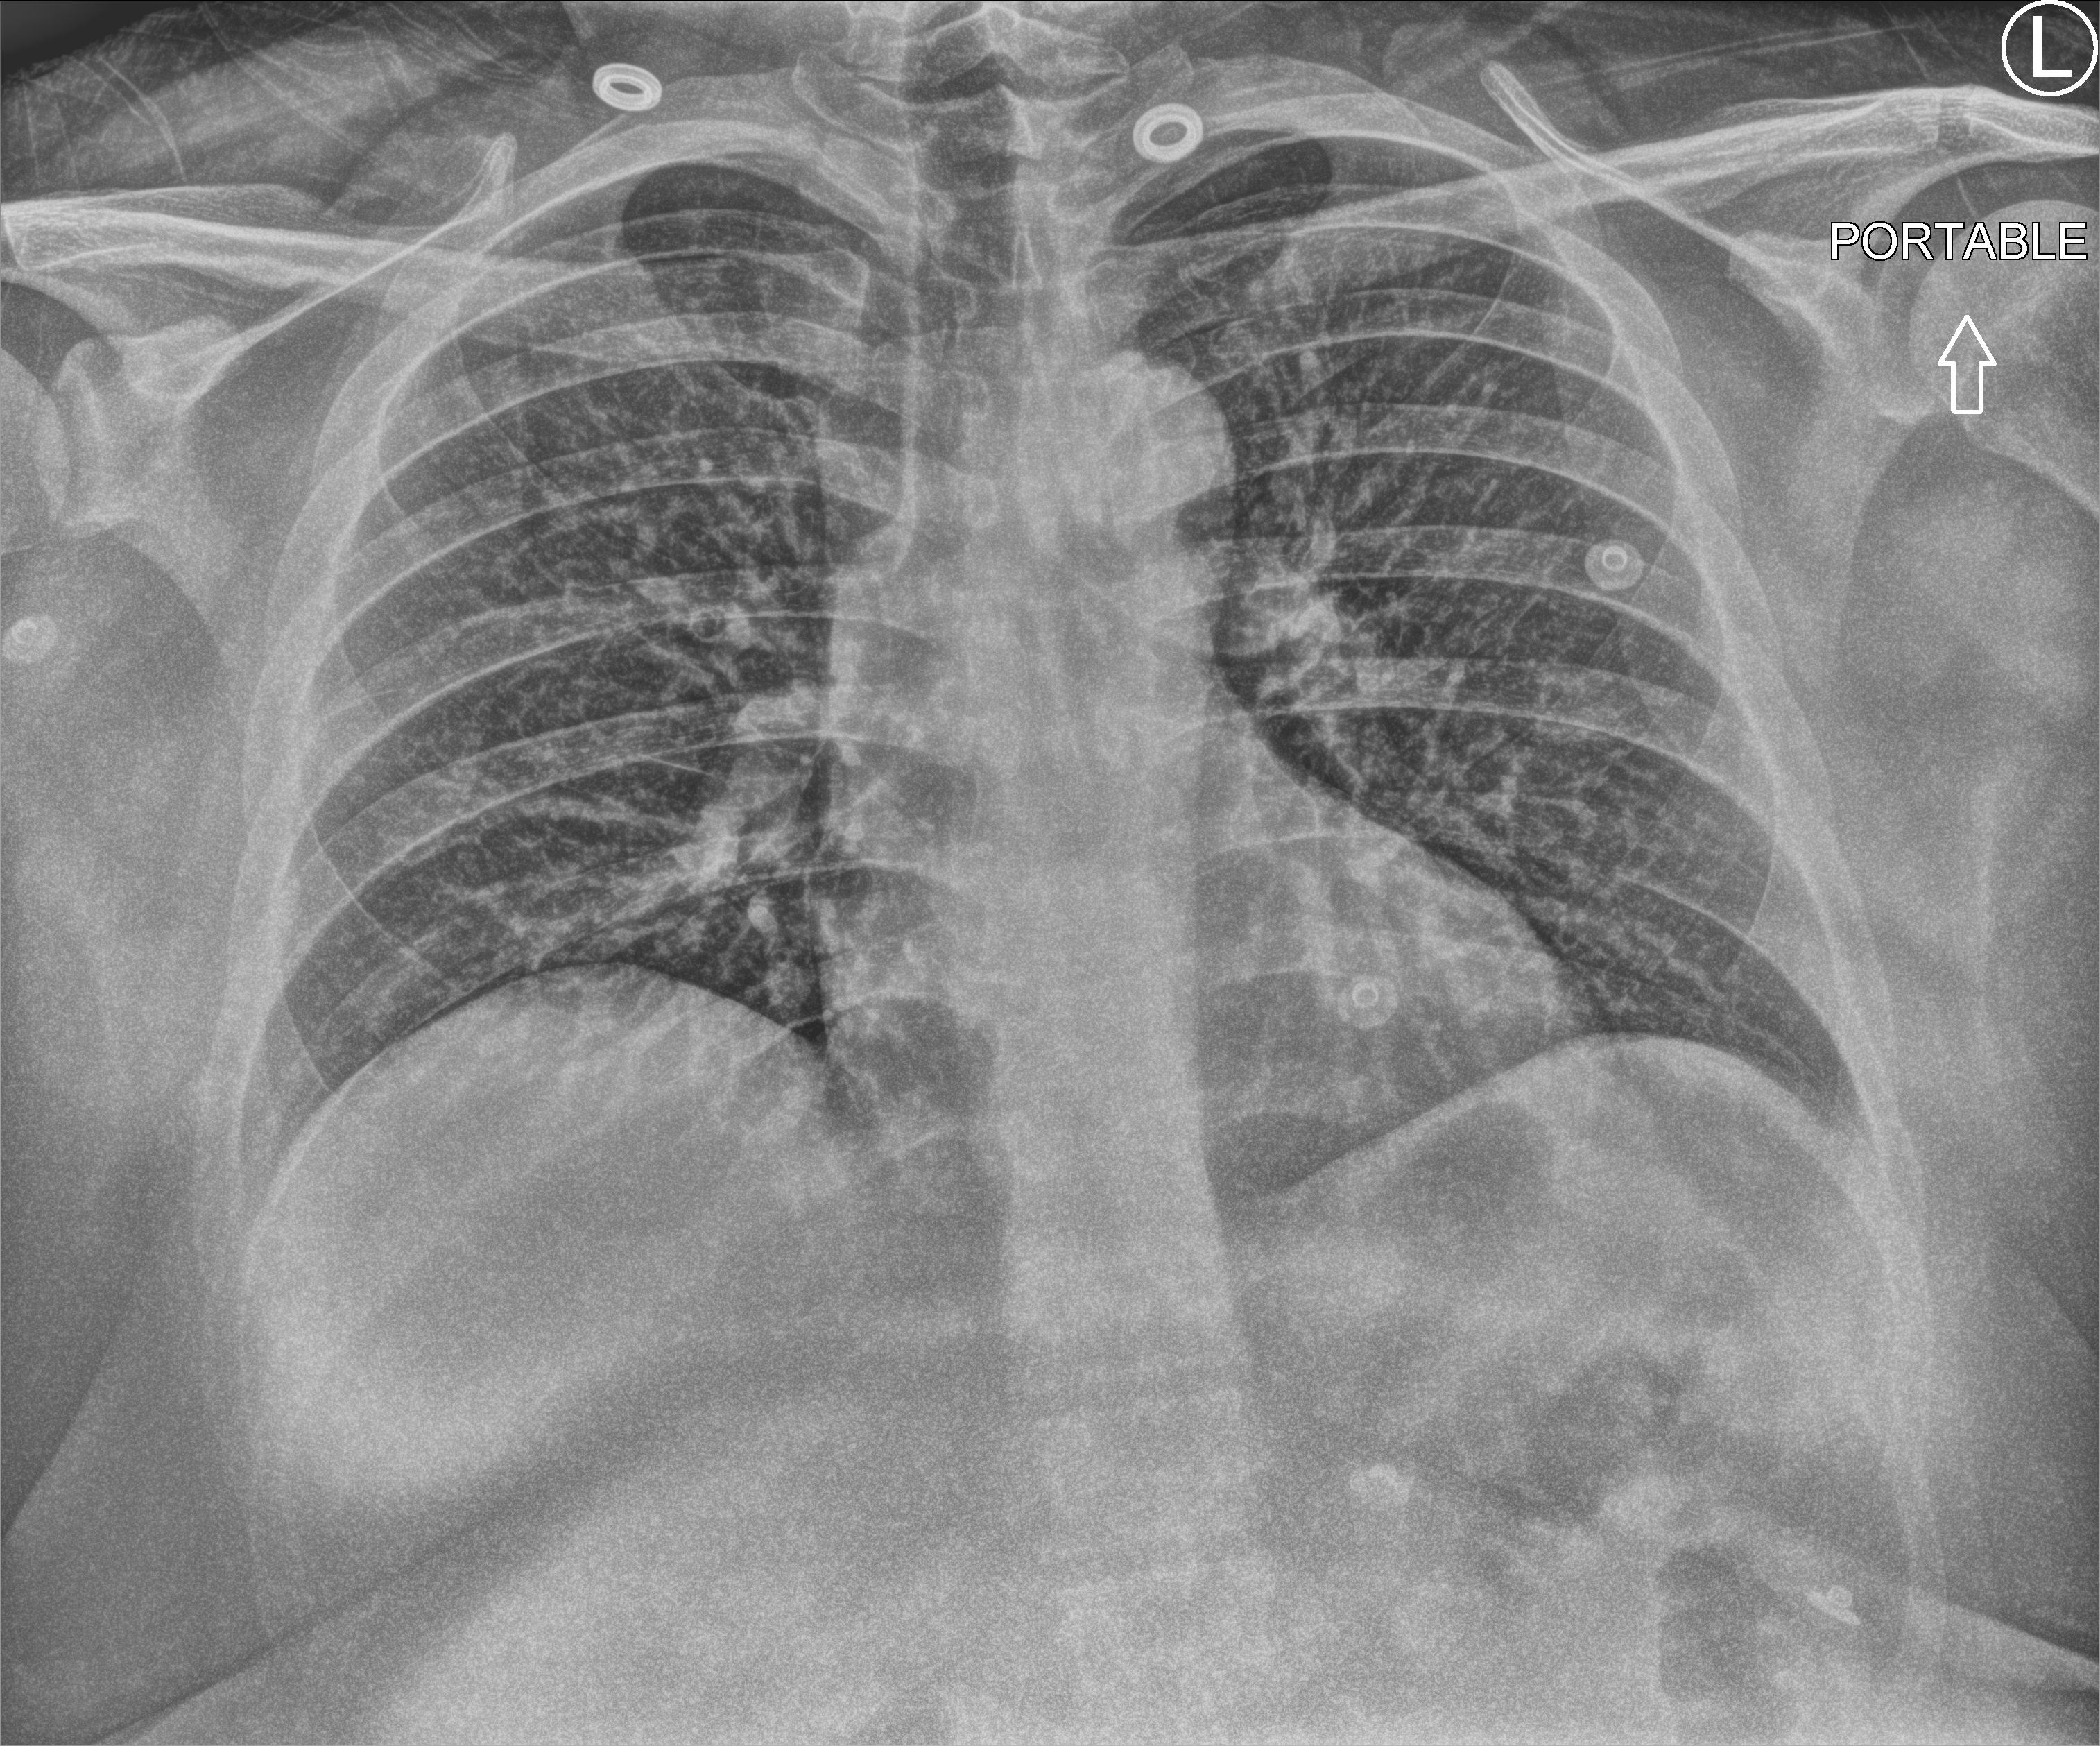
Chest X-ray (portable), anteroposterior (AP) projection. Patient hospitalised with COVID-19; male, aged 18–59 years.
Hospital-stay facts (about this admission, not read from this image; timing relative to this image not recorded): other chronic lung disease (admission record): no.